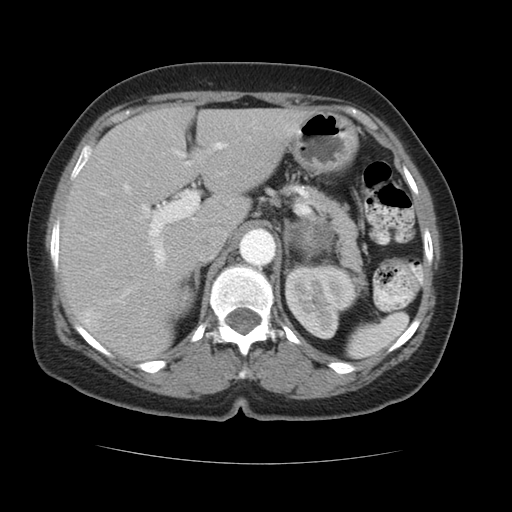
Contrast-enhanced abdominal CT, one axial slice; reconstruction kernel STANDARD; 120 kVp; soft-tissue window (W 400 / L 40 HU); 5 mm slice thickness; 512 × 512 image matrix, field of view 348 × 348 mm. Patient: female, 66 years. From the clinical record (not read from this slice): diagnosis: adrenocortical carcinoma; tumour side: left adrenal; tumour size at pathology: 5.5 cm; Ki-67 index: 15 %; stage (as recorded): 3.
Structures marked on this image (semi-automatic segmentation, software-assisted and operator-edited):
- mass: bounding box <293,220,332,258> (left, top, right, bottom; pixels)